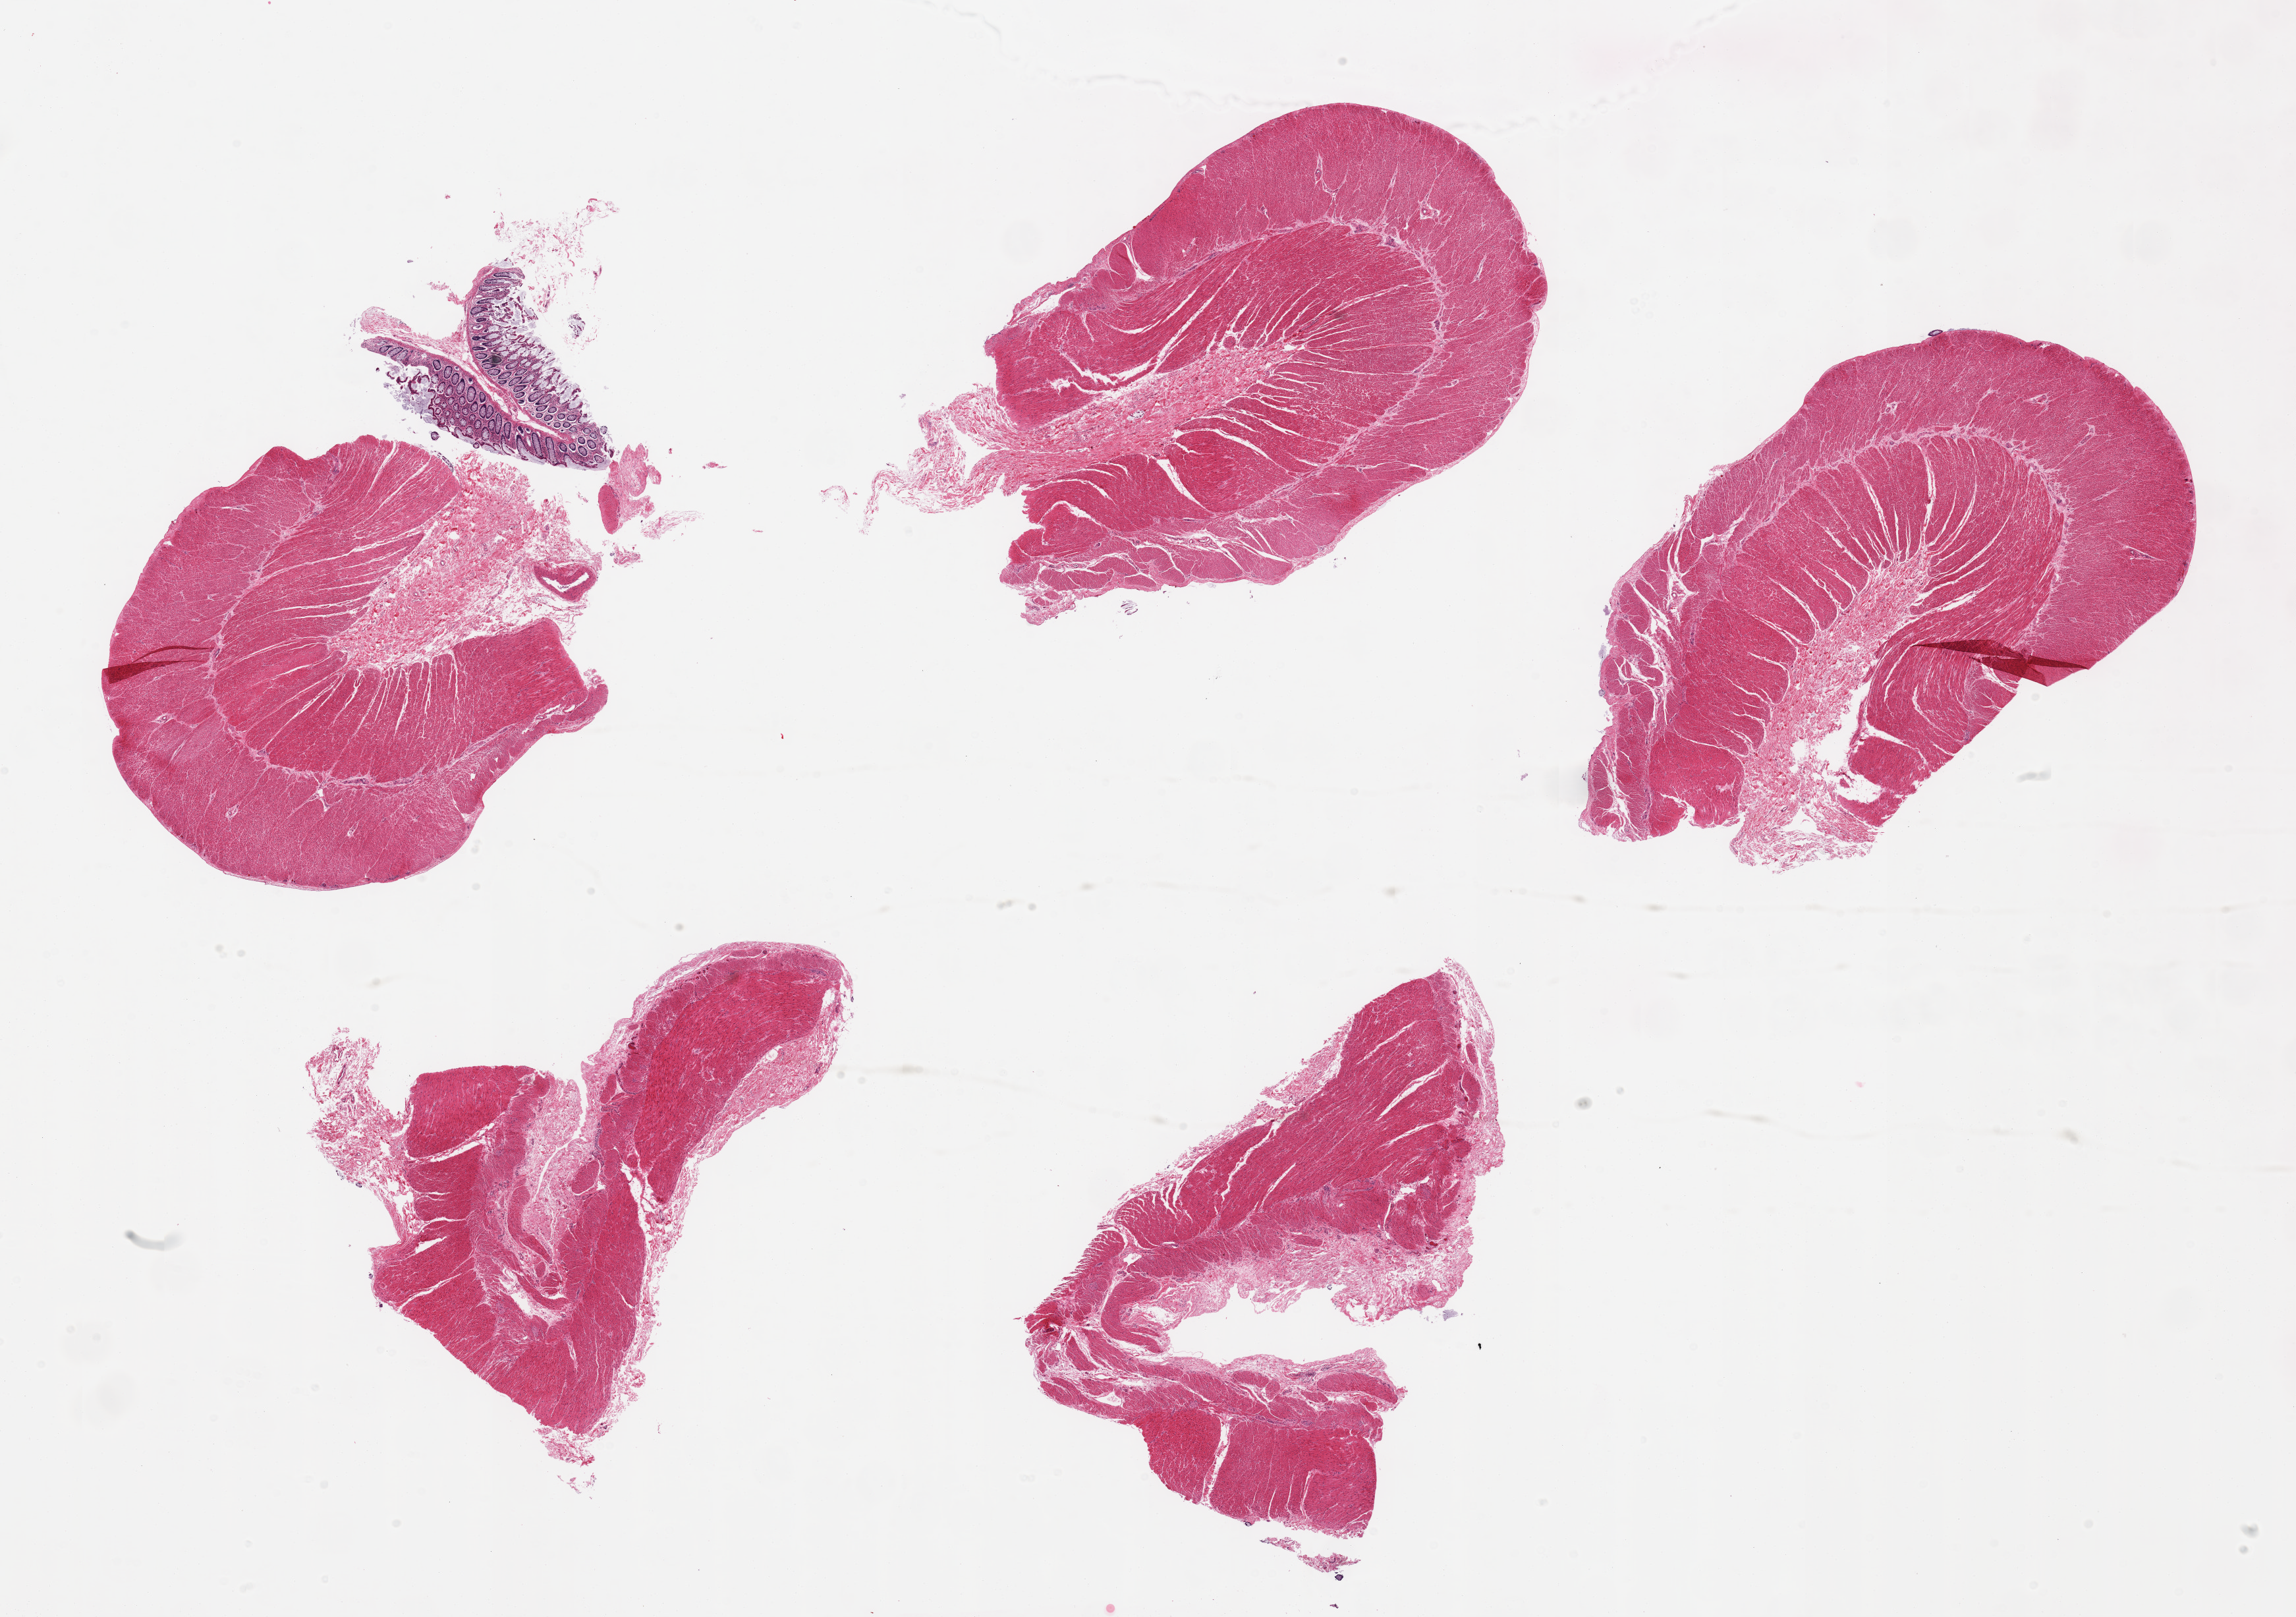
Digitized hematoxylin and eosin (H&E)-stained section, a low-resolution overview of the entire scanned area, about 27.6 x 19.4 mm; PAXgene-fixed paraffin-embedded (PFPE) section; section of transverse colon (target tissue); tissue donor sample.
Reviewer comment on this tissue sample: 5 pieces; only tiny unattached fragment of colonic mucosa; mainly muscularis.